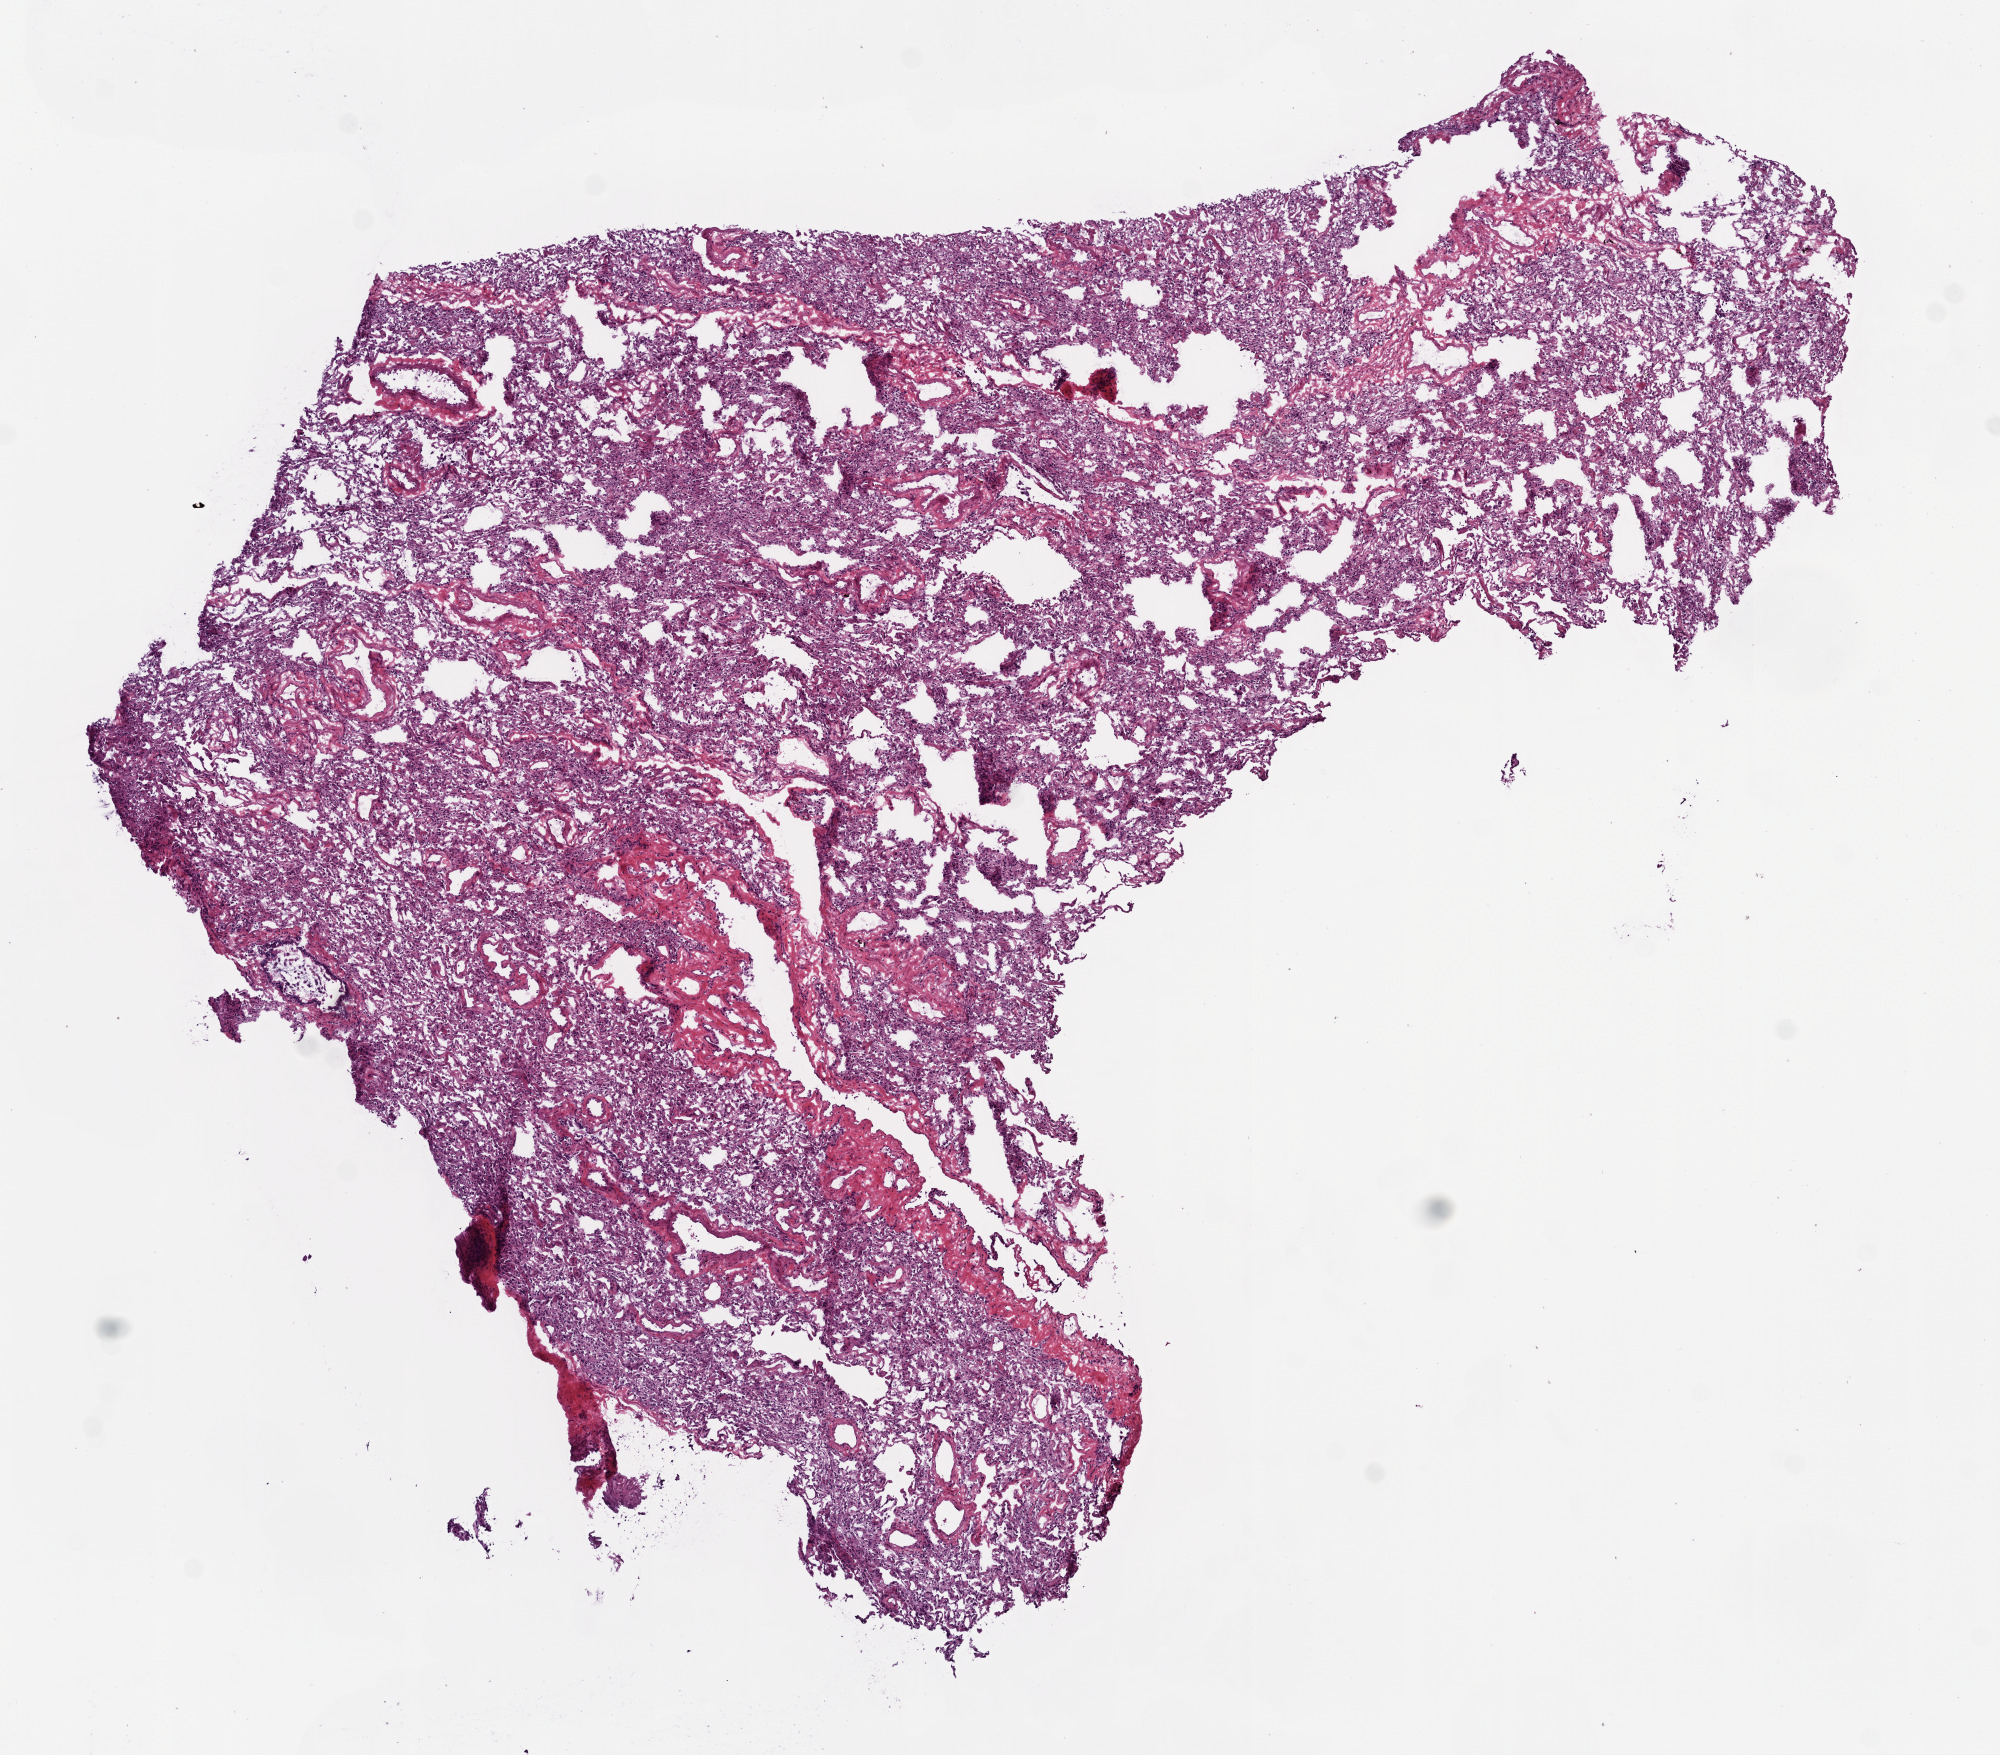
Digitized Hematoxylin and eosin (H&E) stained tissue section (whole slide), whole scanned area (about 8.0 x 7.0 mm, acquisition: 20x scan) shown as a low-resolution overview; frozen section; sample: solid tissue normal (non-tumour tissue), lung. Male, age 57 years at initial diagnosis.
This section: solid tissue normal (non-tumour) sample from the same patient. Patient diagnosis: Squamous cell carcinoma, NOS (lower lobe, lung).